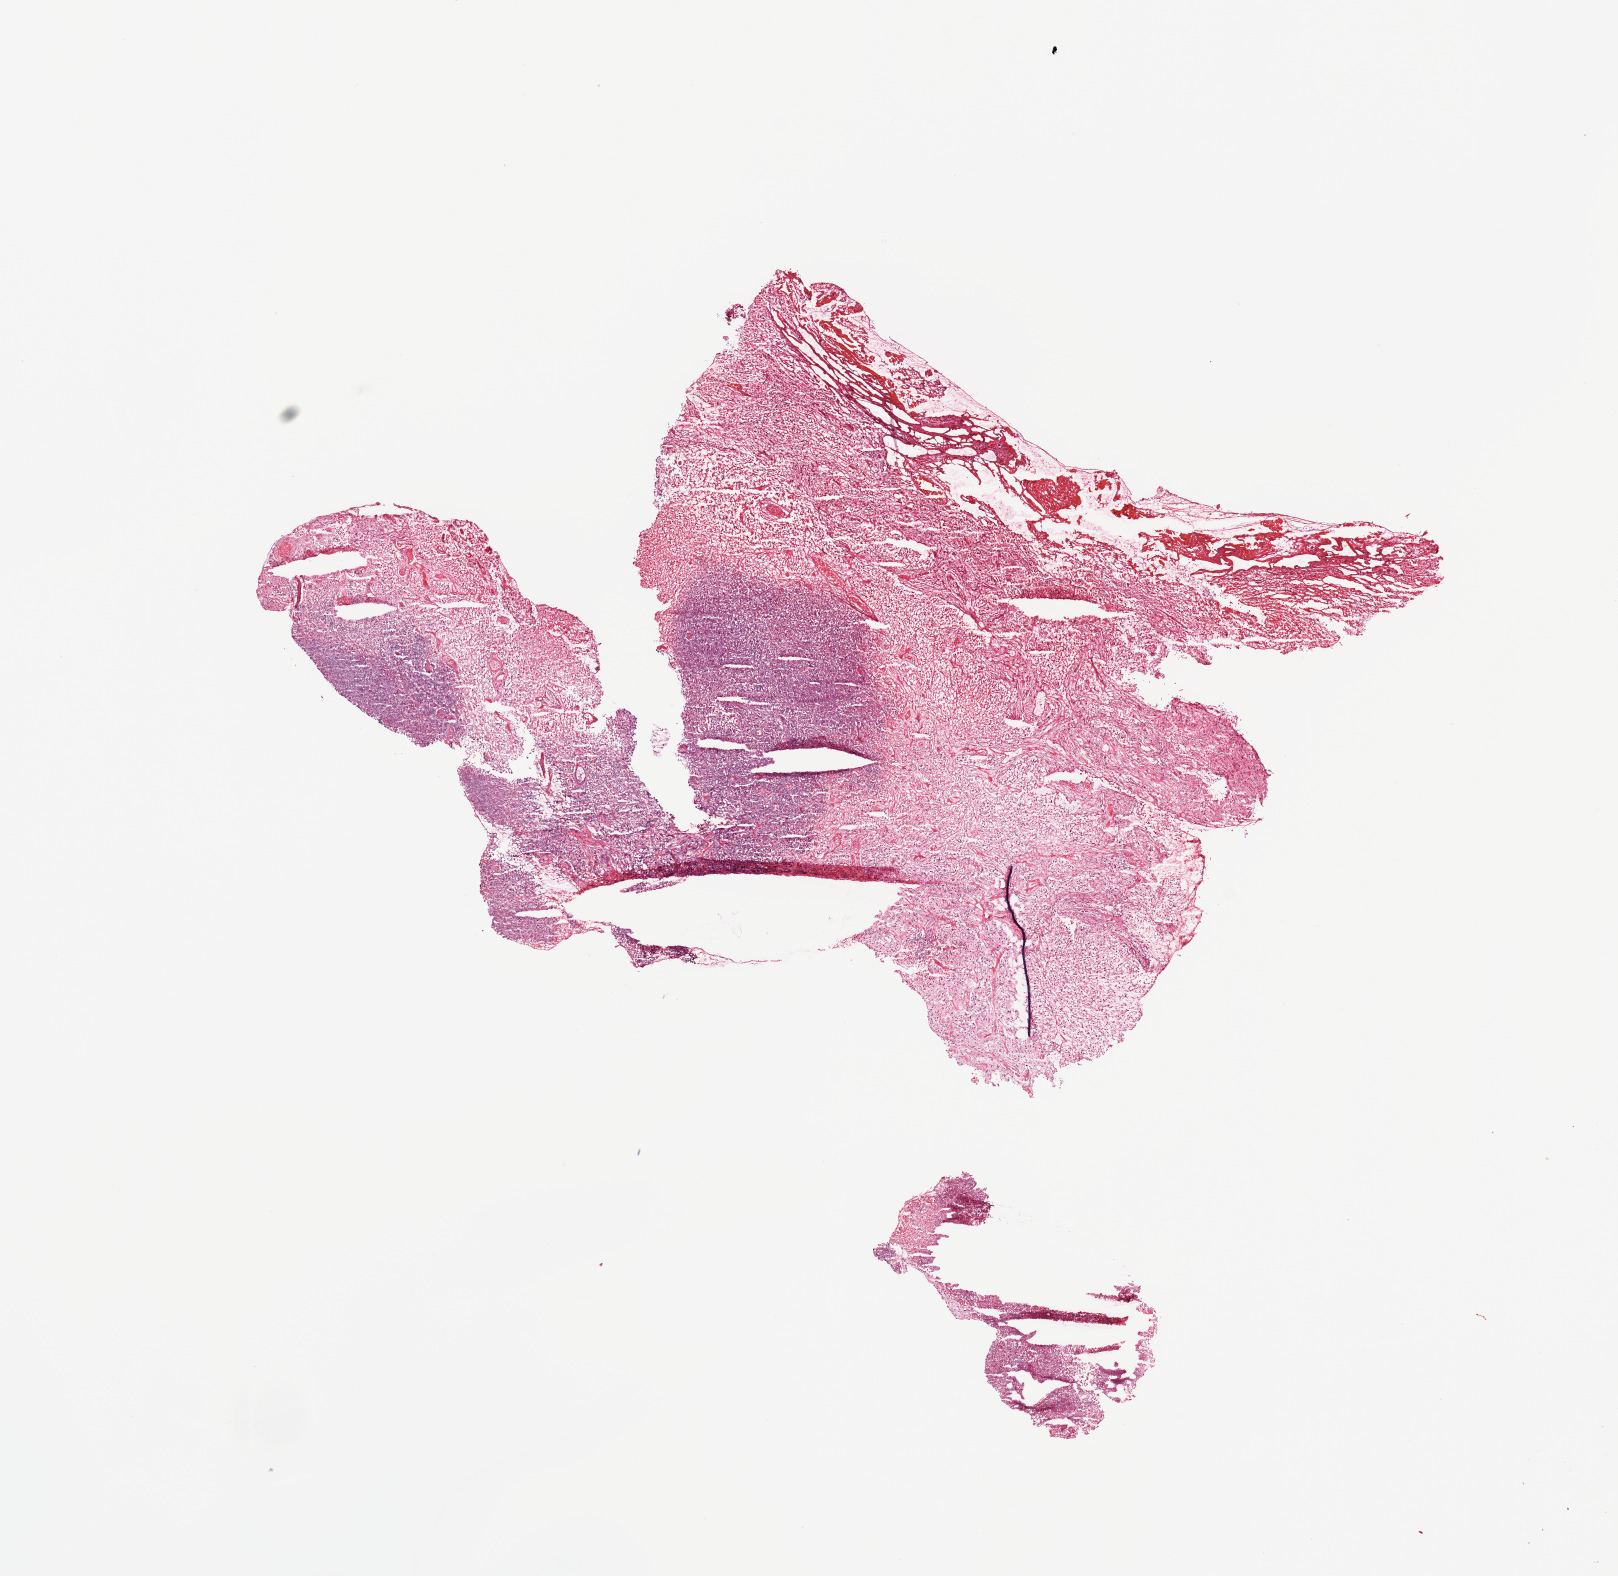
H&E whole-slide image, low-resolution overview of the scanned area, about 12.8 x 12.5 mm, brain, tumour tissue. Female, 74 y/o.
Primary tumour site (as recorded): temporal lobe. Patient diagnosis (cohort enrolment): glioblastoma multiforme (brain).